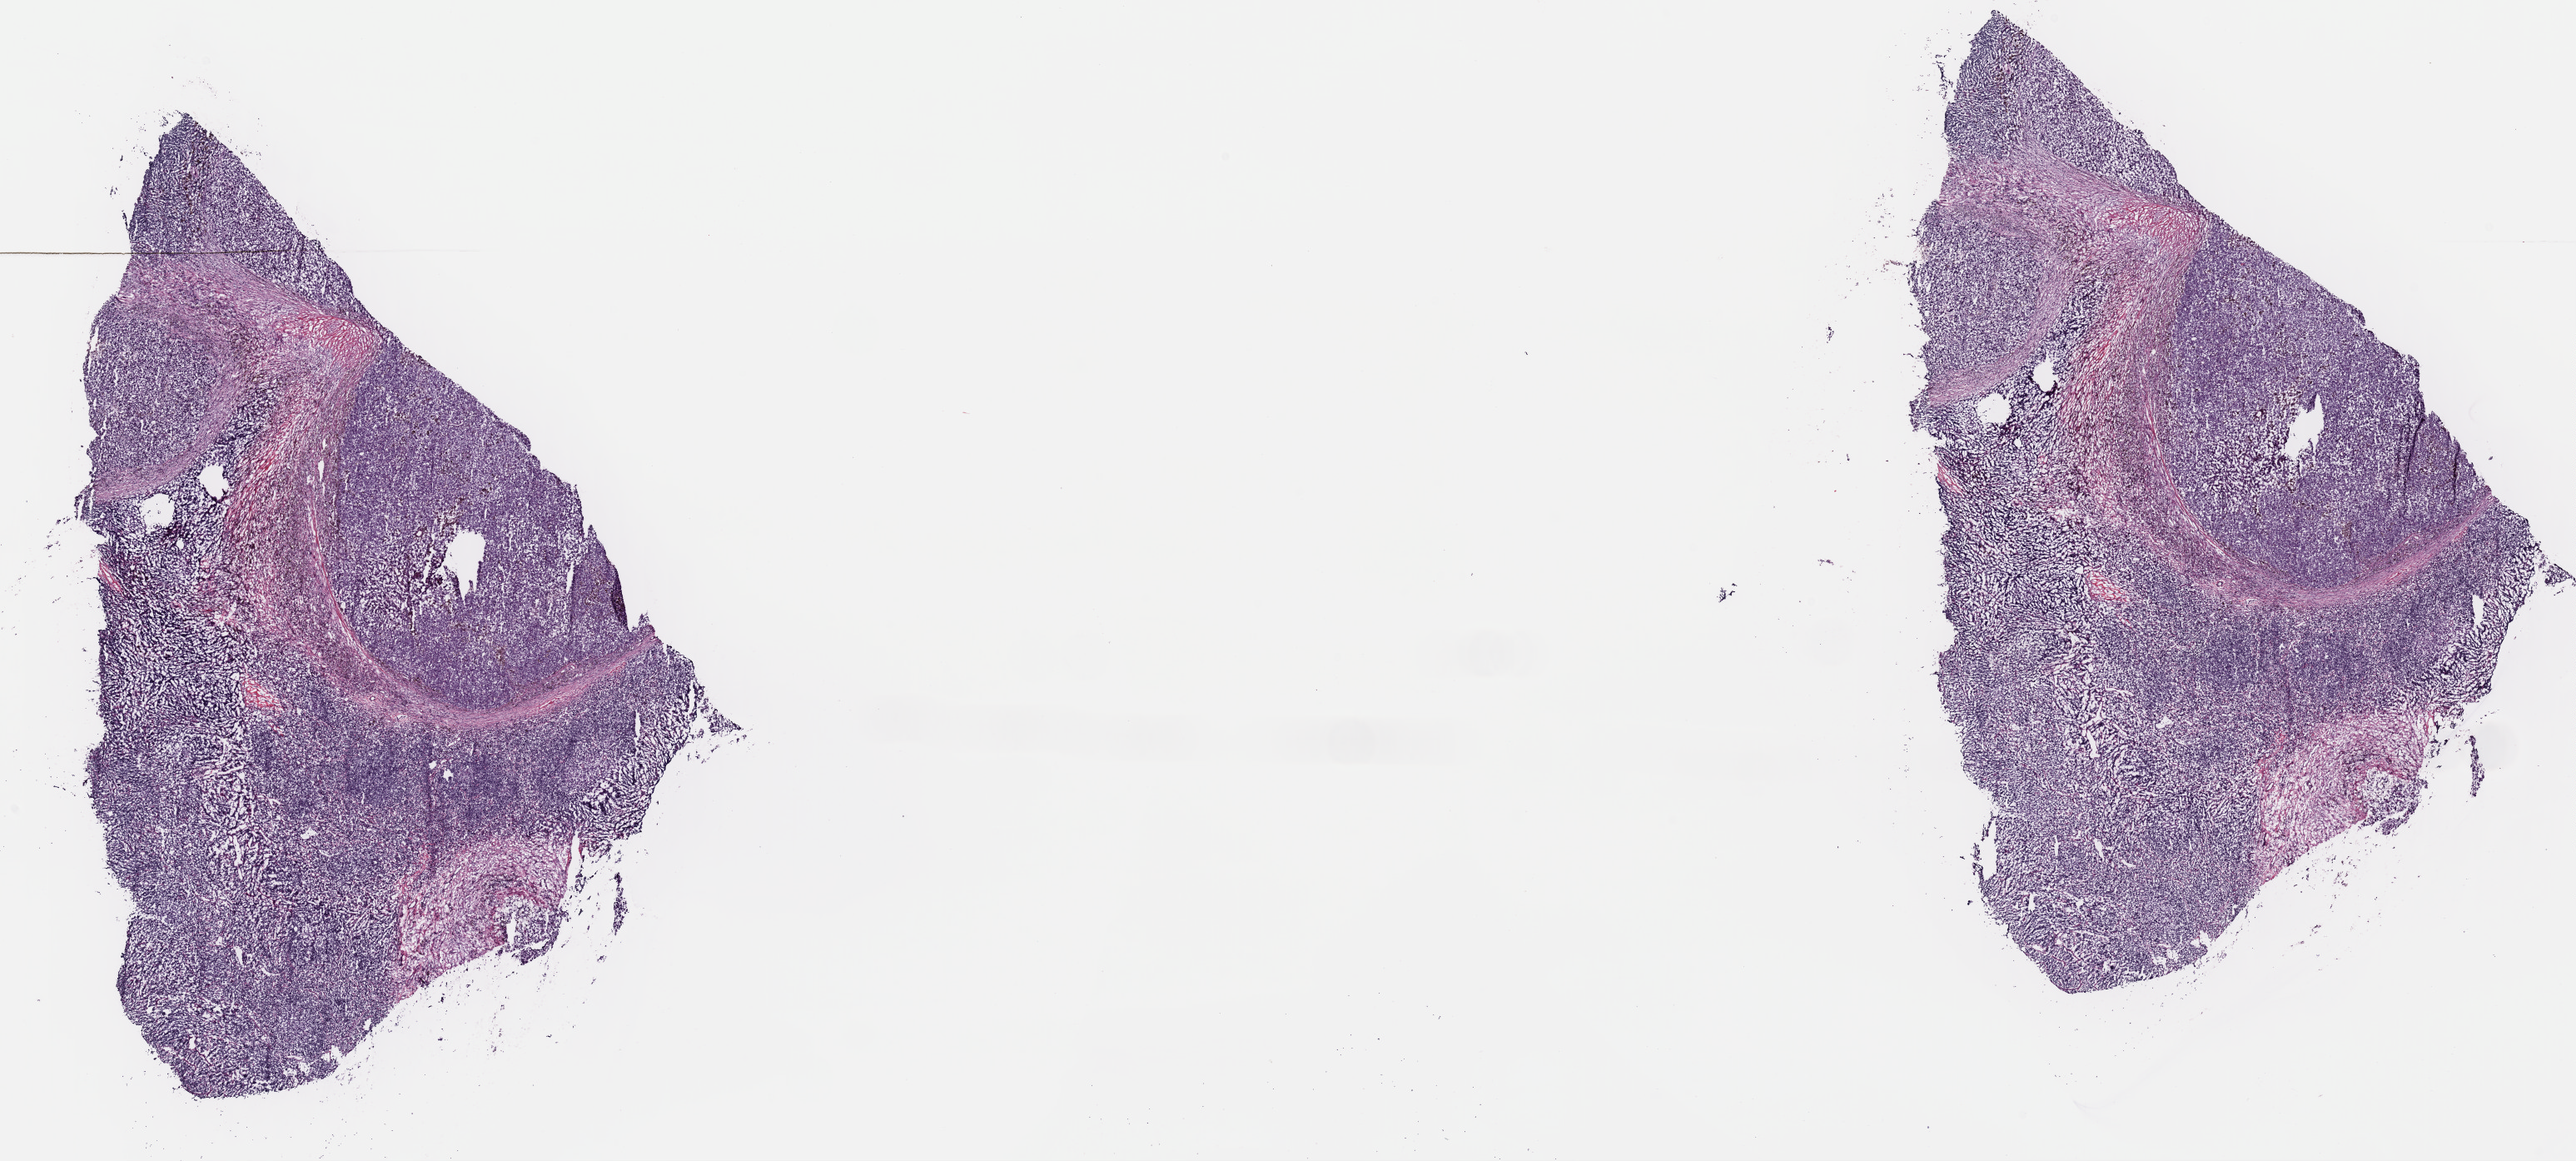
Whole-slide histology image, Hematoxylin and eosin (H&E) stained — shown as a low-resolution overview of the whole scanned area (about 24.4 x 11.0 mm, slide scanned at 40x), frozen section from the top of the tissue portion, metastatic tumour sample, sampled site: lymph nodes of inguinal region or leg. Female, age 46 years at initial diagnosis. Pathologist review of this section (percent, as recorded): tumour cells 100%, tumour nuclei 90%, normal cells 0%, stromal cells 0%, necrosis 0%. Inflammatory infiltration, as recorded: lymphocyte infiltration 0%, monocyte infiltration 0%, neutrophil infiltration 0%.
This section: metastatic tumour tissue. Patient diagnosis: Malignant melanoma, NOS.